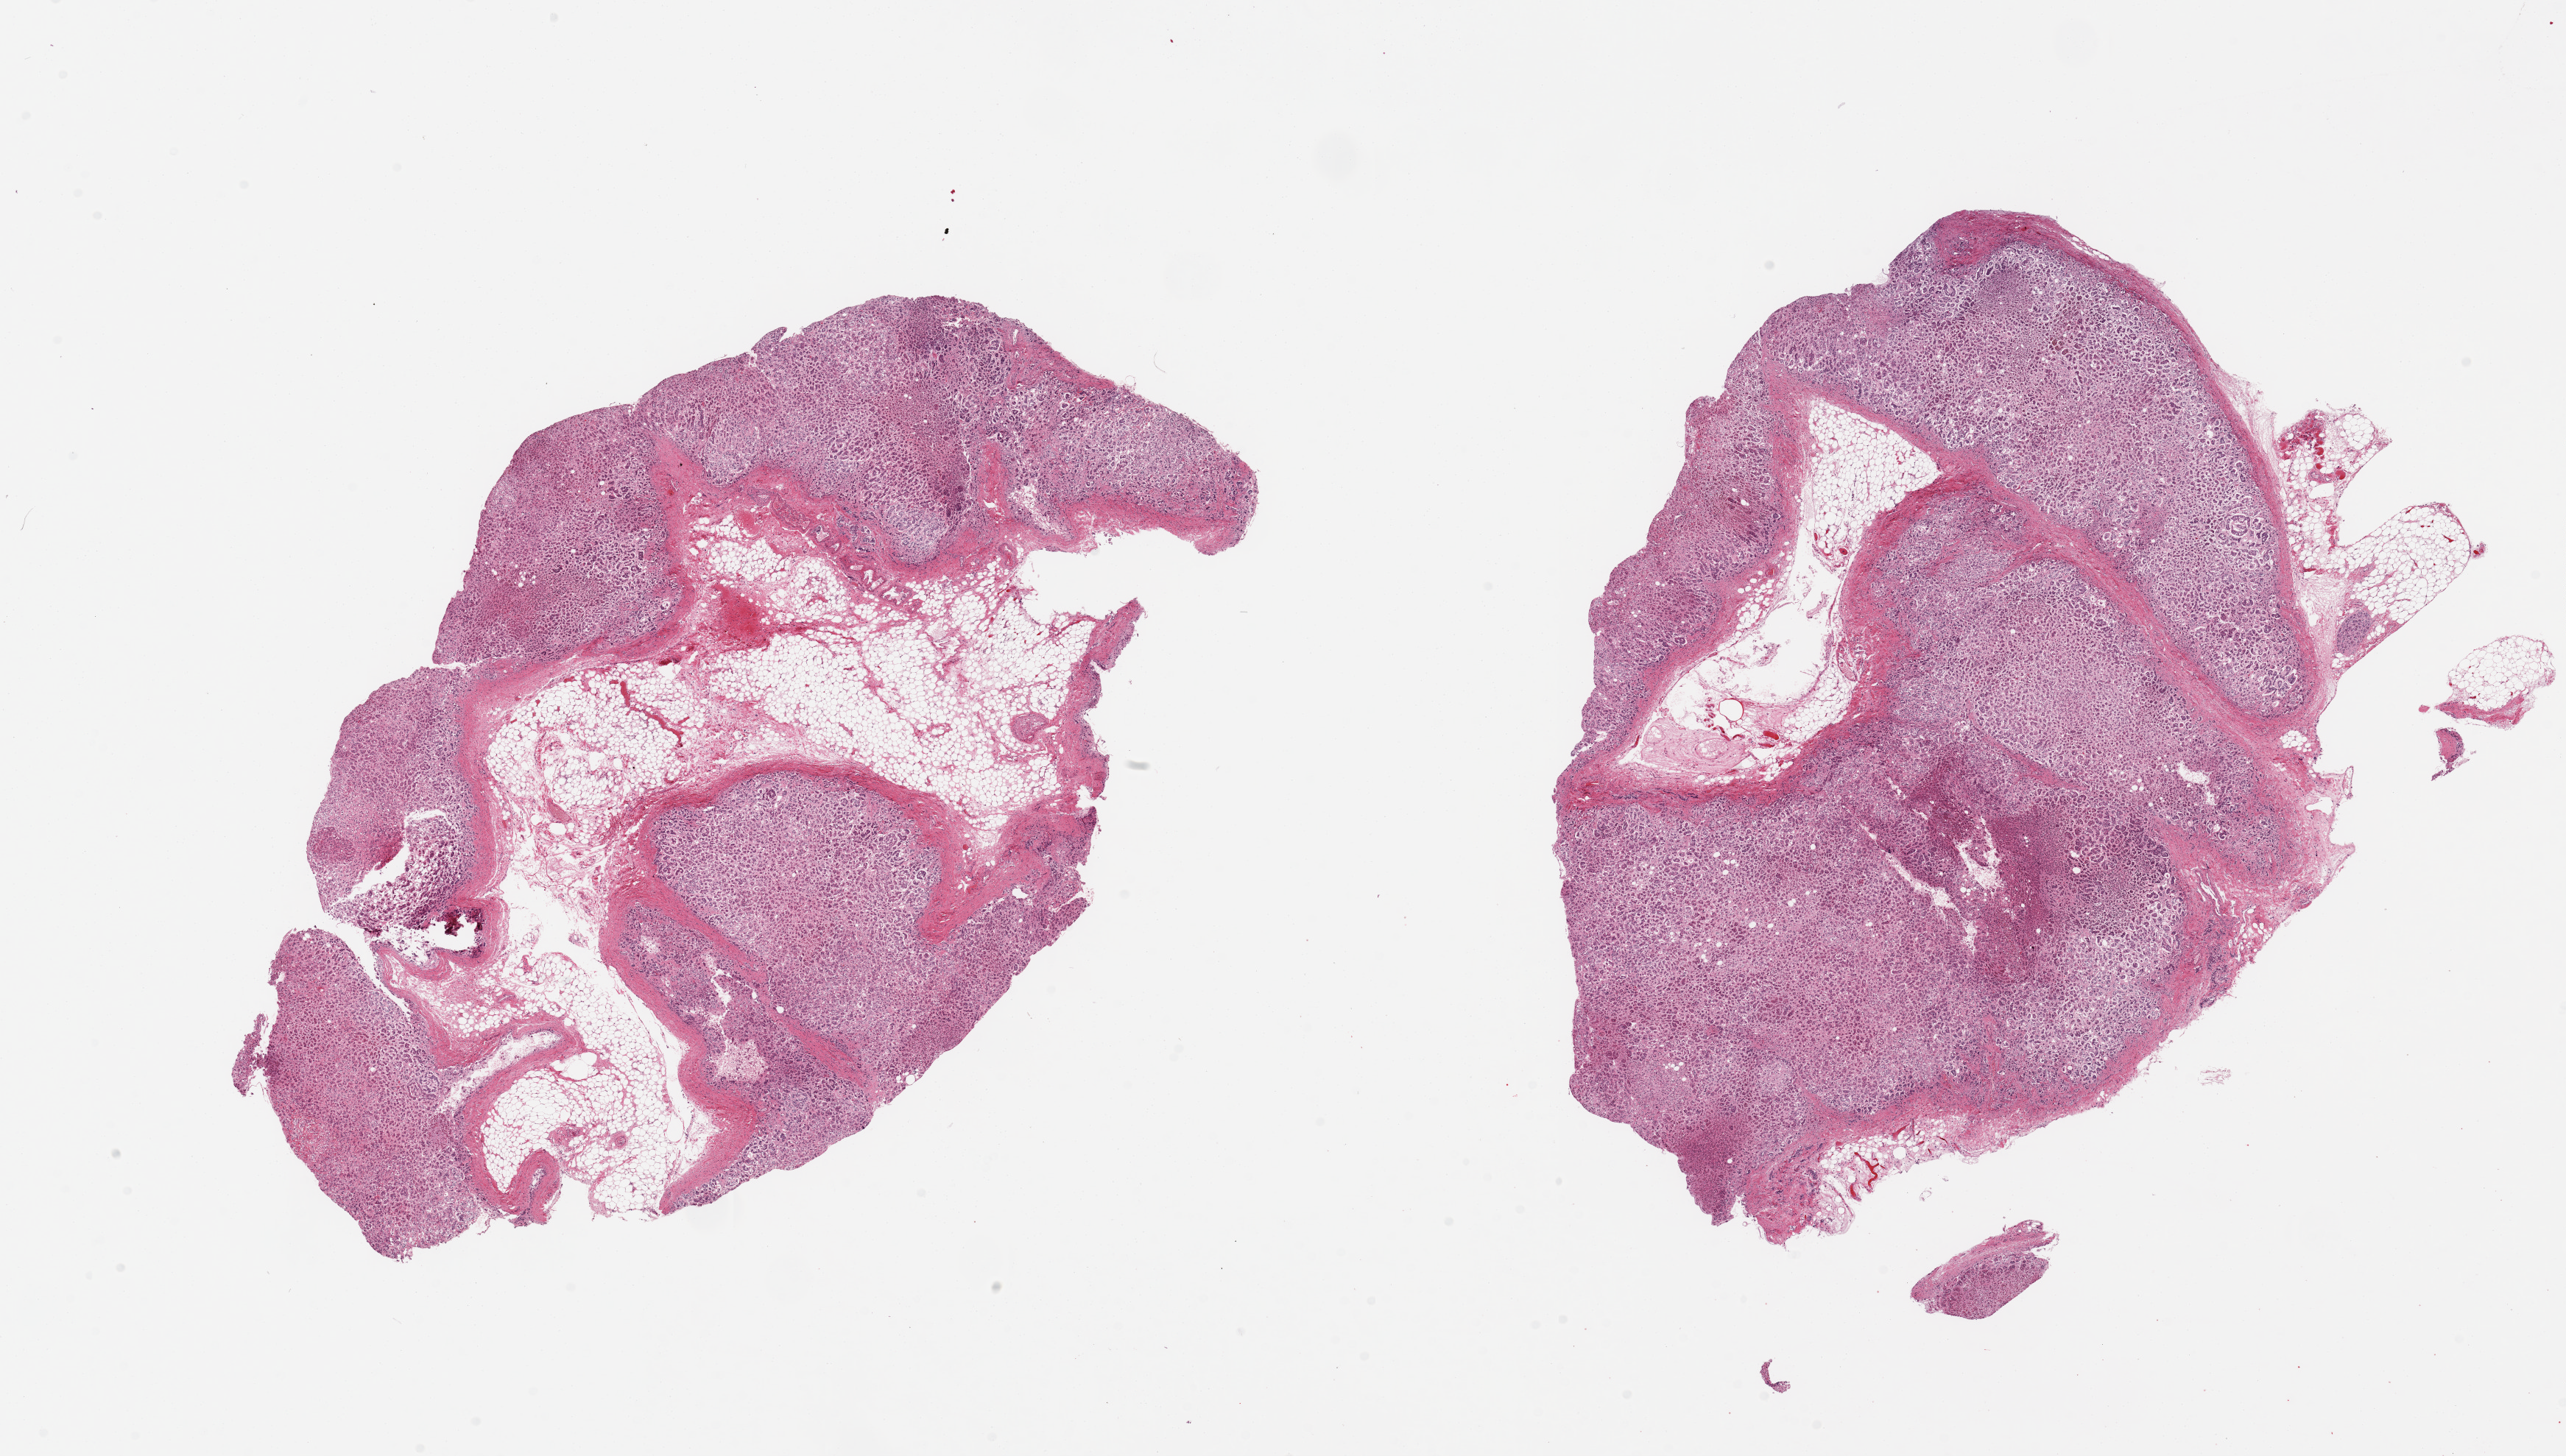
Digitized hematoxylin and eosin (H&E)-stained section — a low-resolution overview of the entire scanned area, about 27.6 x 15.6 mm. PAXgene-fixed paraffin-embedded (PFPE) section. Sampled site (target tissue): adrenal gland. Donor tissue sample. Donor sex: male.
Pathologist's review note for this sample: 2 pieces; 40% & 20% fat content.